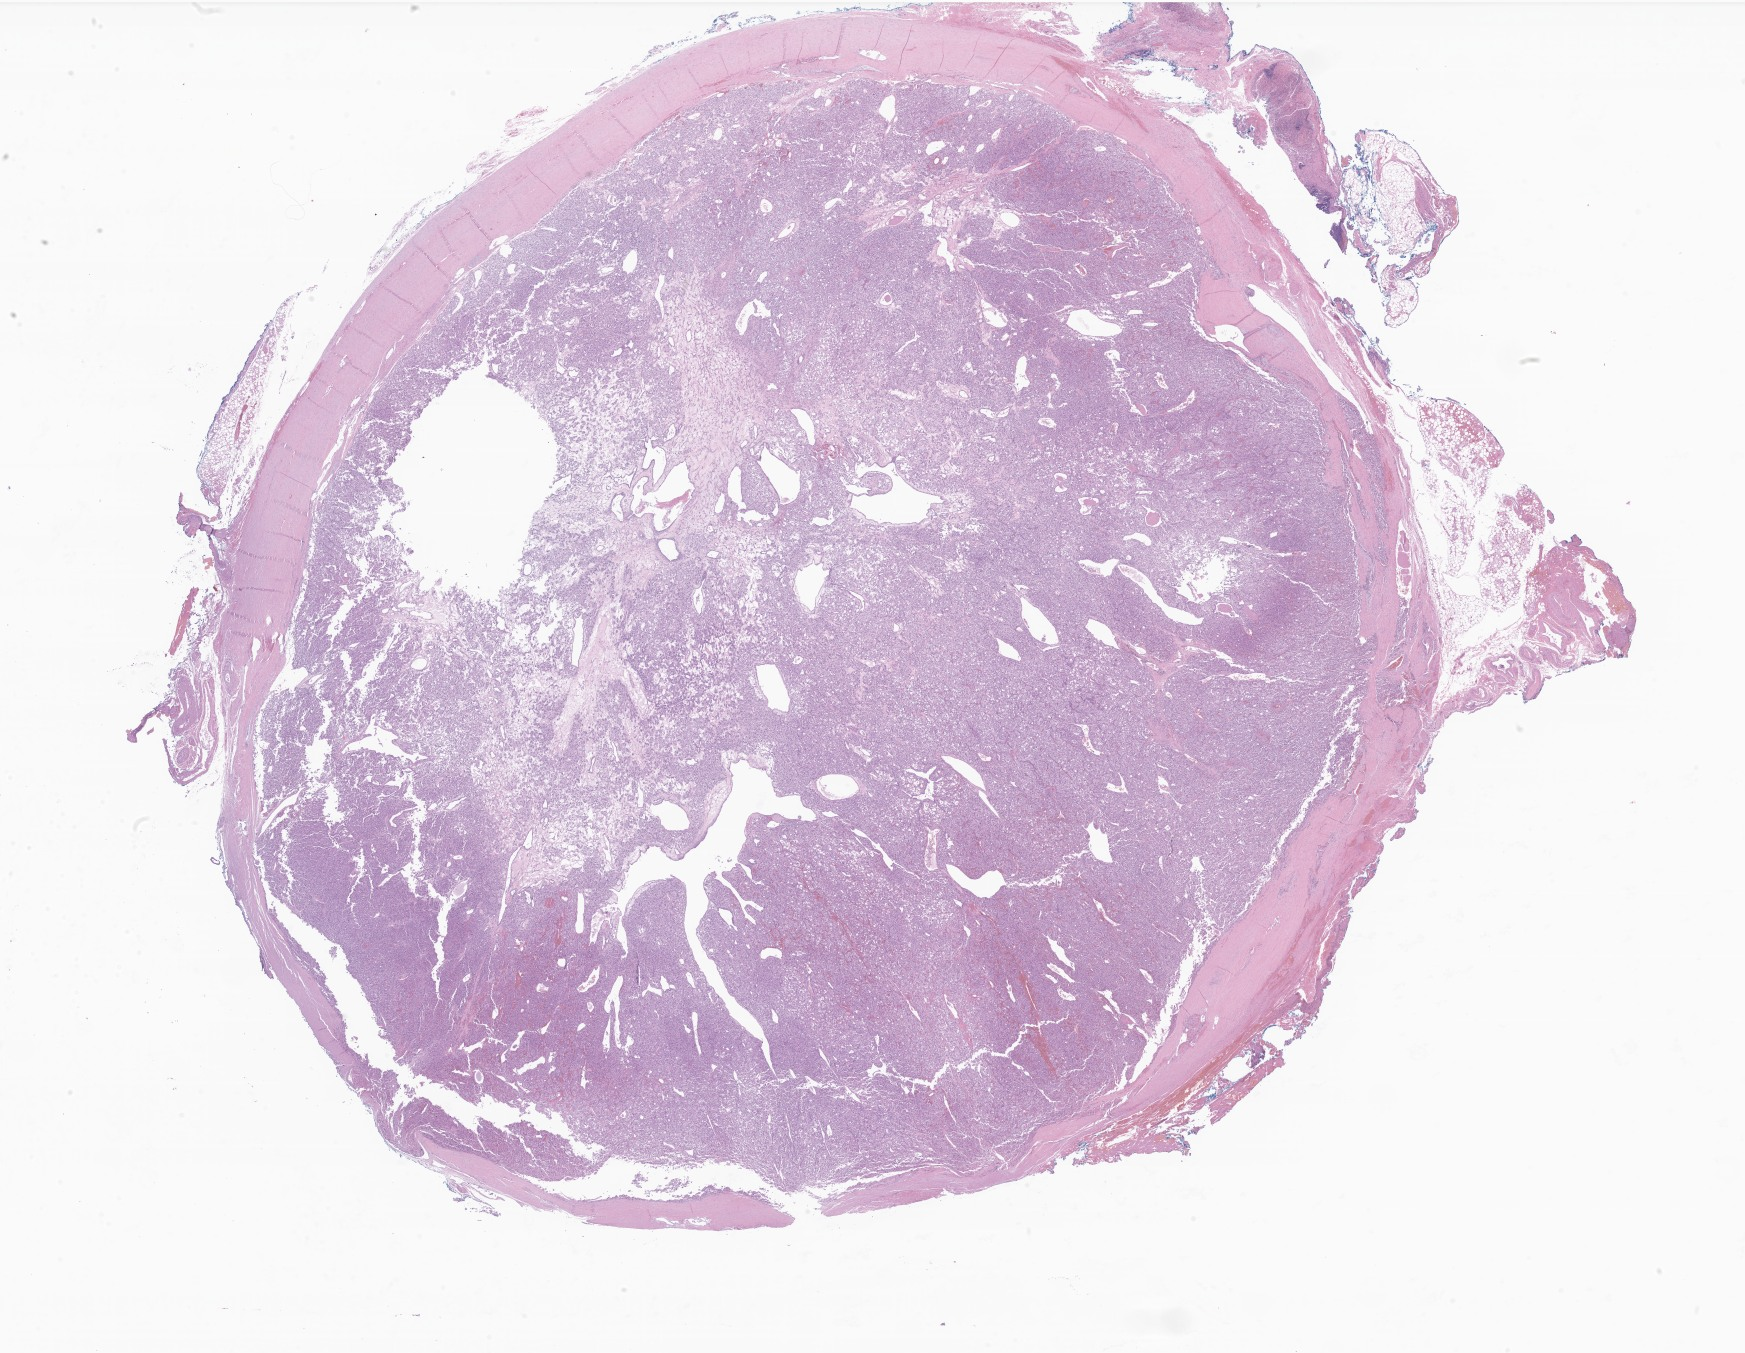
H&E whole-slide image of tumor tissue from the retroperitoneum — low-resolution overview of the scanned area, about 29.4 x 22.8 mm. FFPE section. Patient: male, age 152 months (12 years 8 months).
Diagnosis: Paraganglioma, NOS.